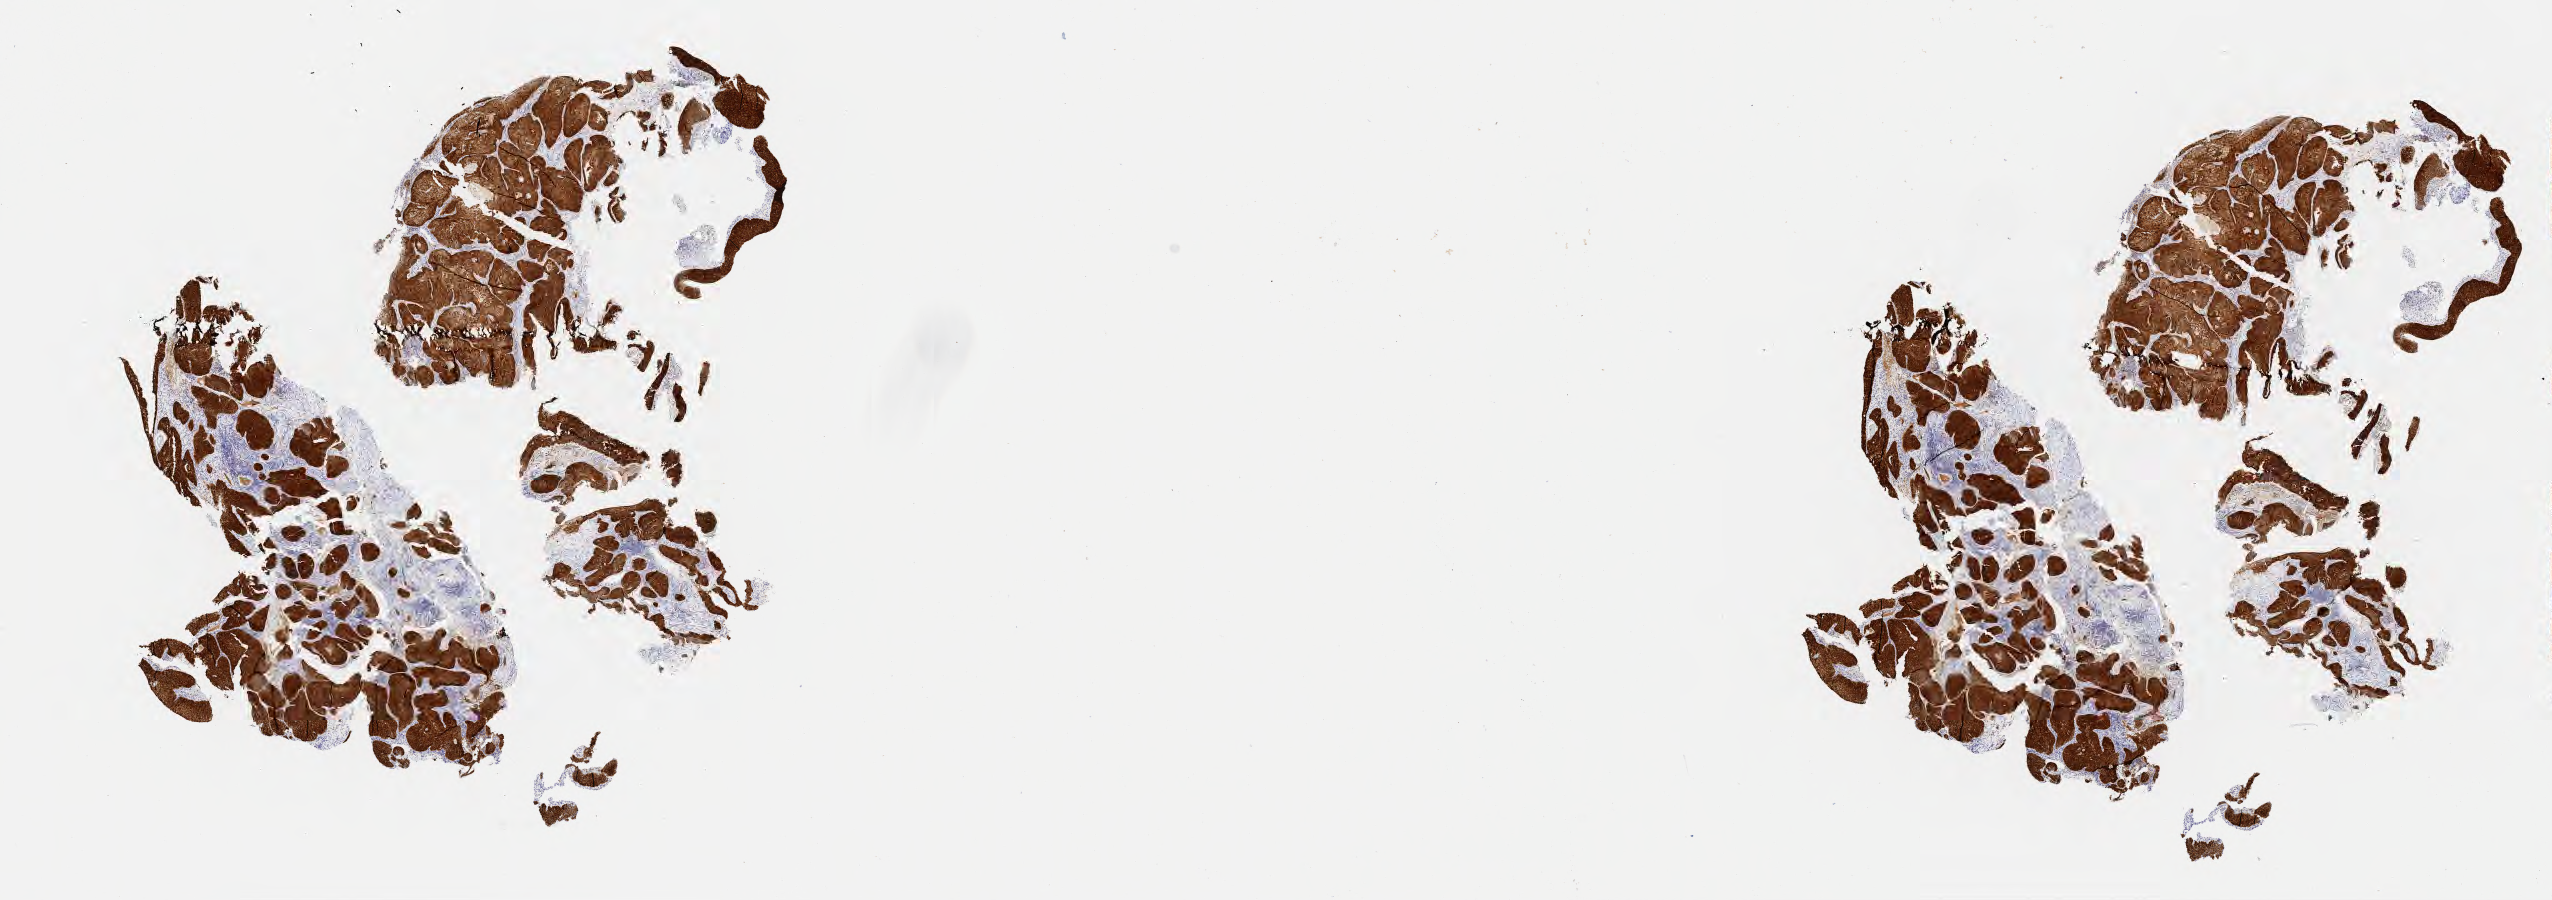
IHC for p16 (p16INK4a), whole-slide image, low-resolution overview of the scanned area, about 20.6 x 7.3 mm; specimen: tumor tissue; site: cervix. Patient female; age 55 years.
Diagnosis: Squamous cell carcinoma, large cell, nonkeratinizing, NOS.